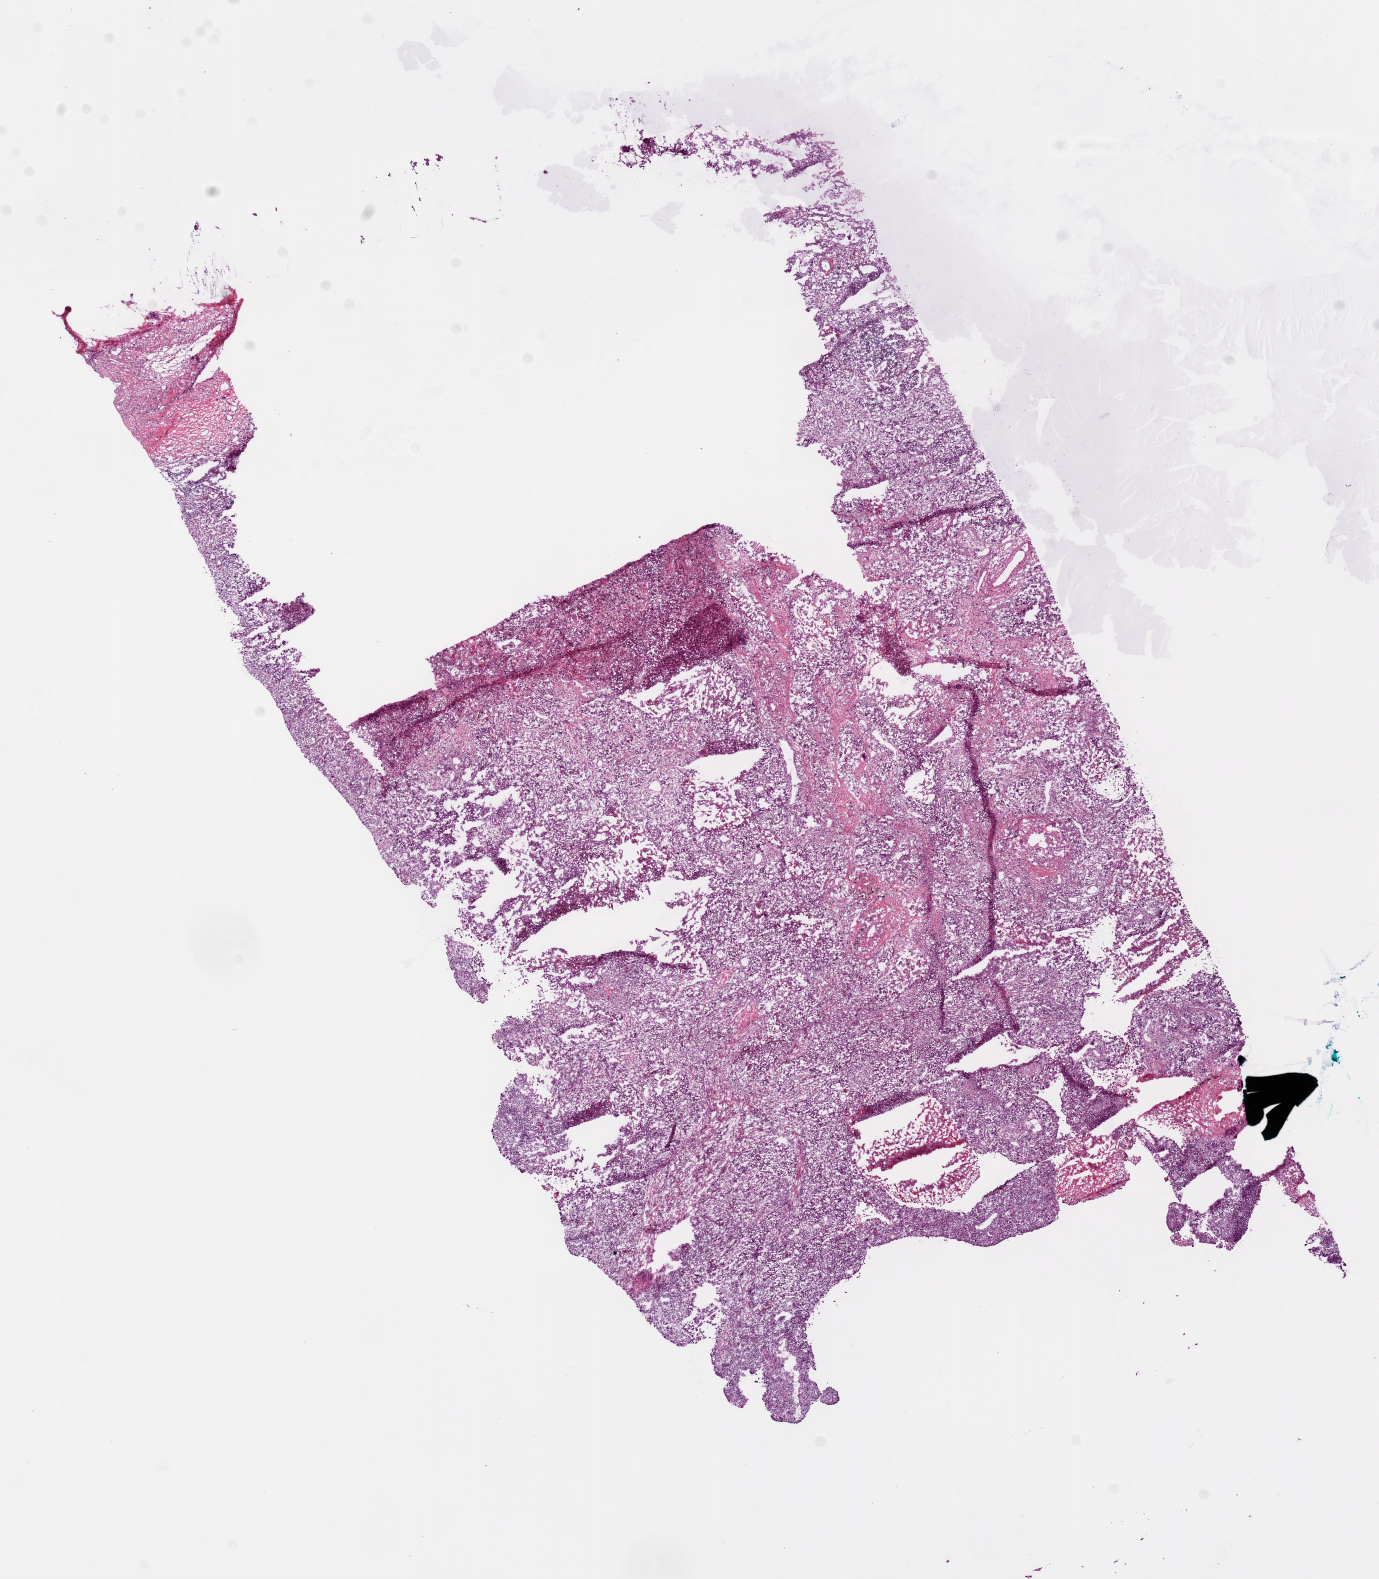
H&E whole-slide image, shown as a low-resolution overview of the whole scanned area (about 11.1 x 12.7 mm, acquisition: 20x scan), frozen section from the bottom of the tissue portion, sample: primary tumour, lung. Female, age 80 years at initial diagnosis. Slide review estimates, as recorded: tumour nuclei 70%, necrosis 0%.
AJCC pathologic stage: IB. Laterality: right. Pathologic diagnosis: Squamous cell carcinoma, NOS.